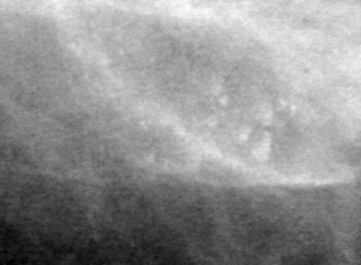
Cropped region of a digitized screen-film mammogram centred on a radiologist-marked abnormality, right breast, MLO view.
Marked abnormality: calcifications, morphology pleomorphic, distribution clustered; BI-RADS assessment category 4; pathology (as recorded): malignant.